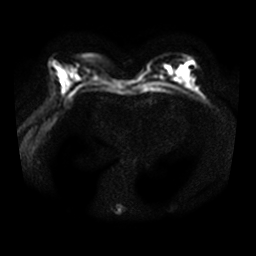
Breast MRI, one axial slice. Slice 17 of 34 in the series (ordered by position). Diffusion-weighted series; image 2 of 4 stored at this slice position (different b-values; order by instance number). 3 T. 256 × 256 image matrix. Female patient.
Outlined on this slice (manually delineated by an expert):
- tumour on diffusion-weighted imaging: box from (x=180, y=66) to (x=189, y=76) px